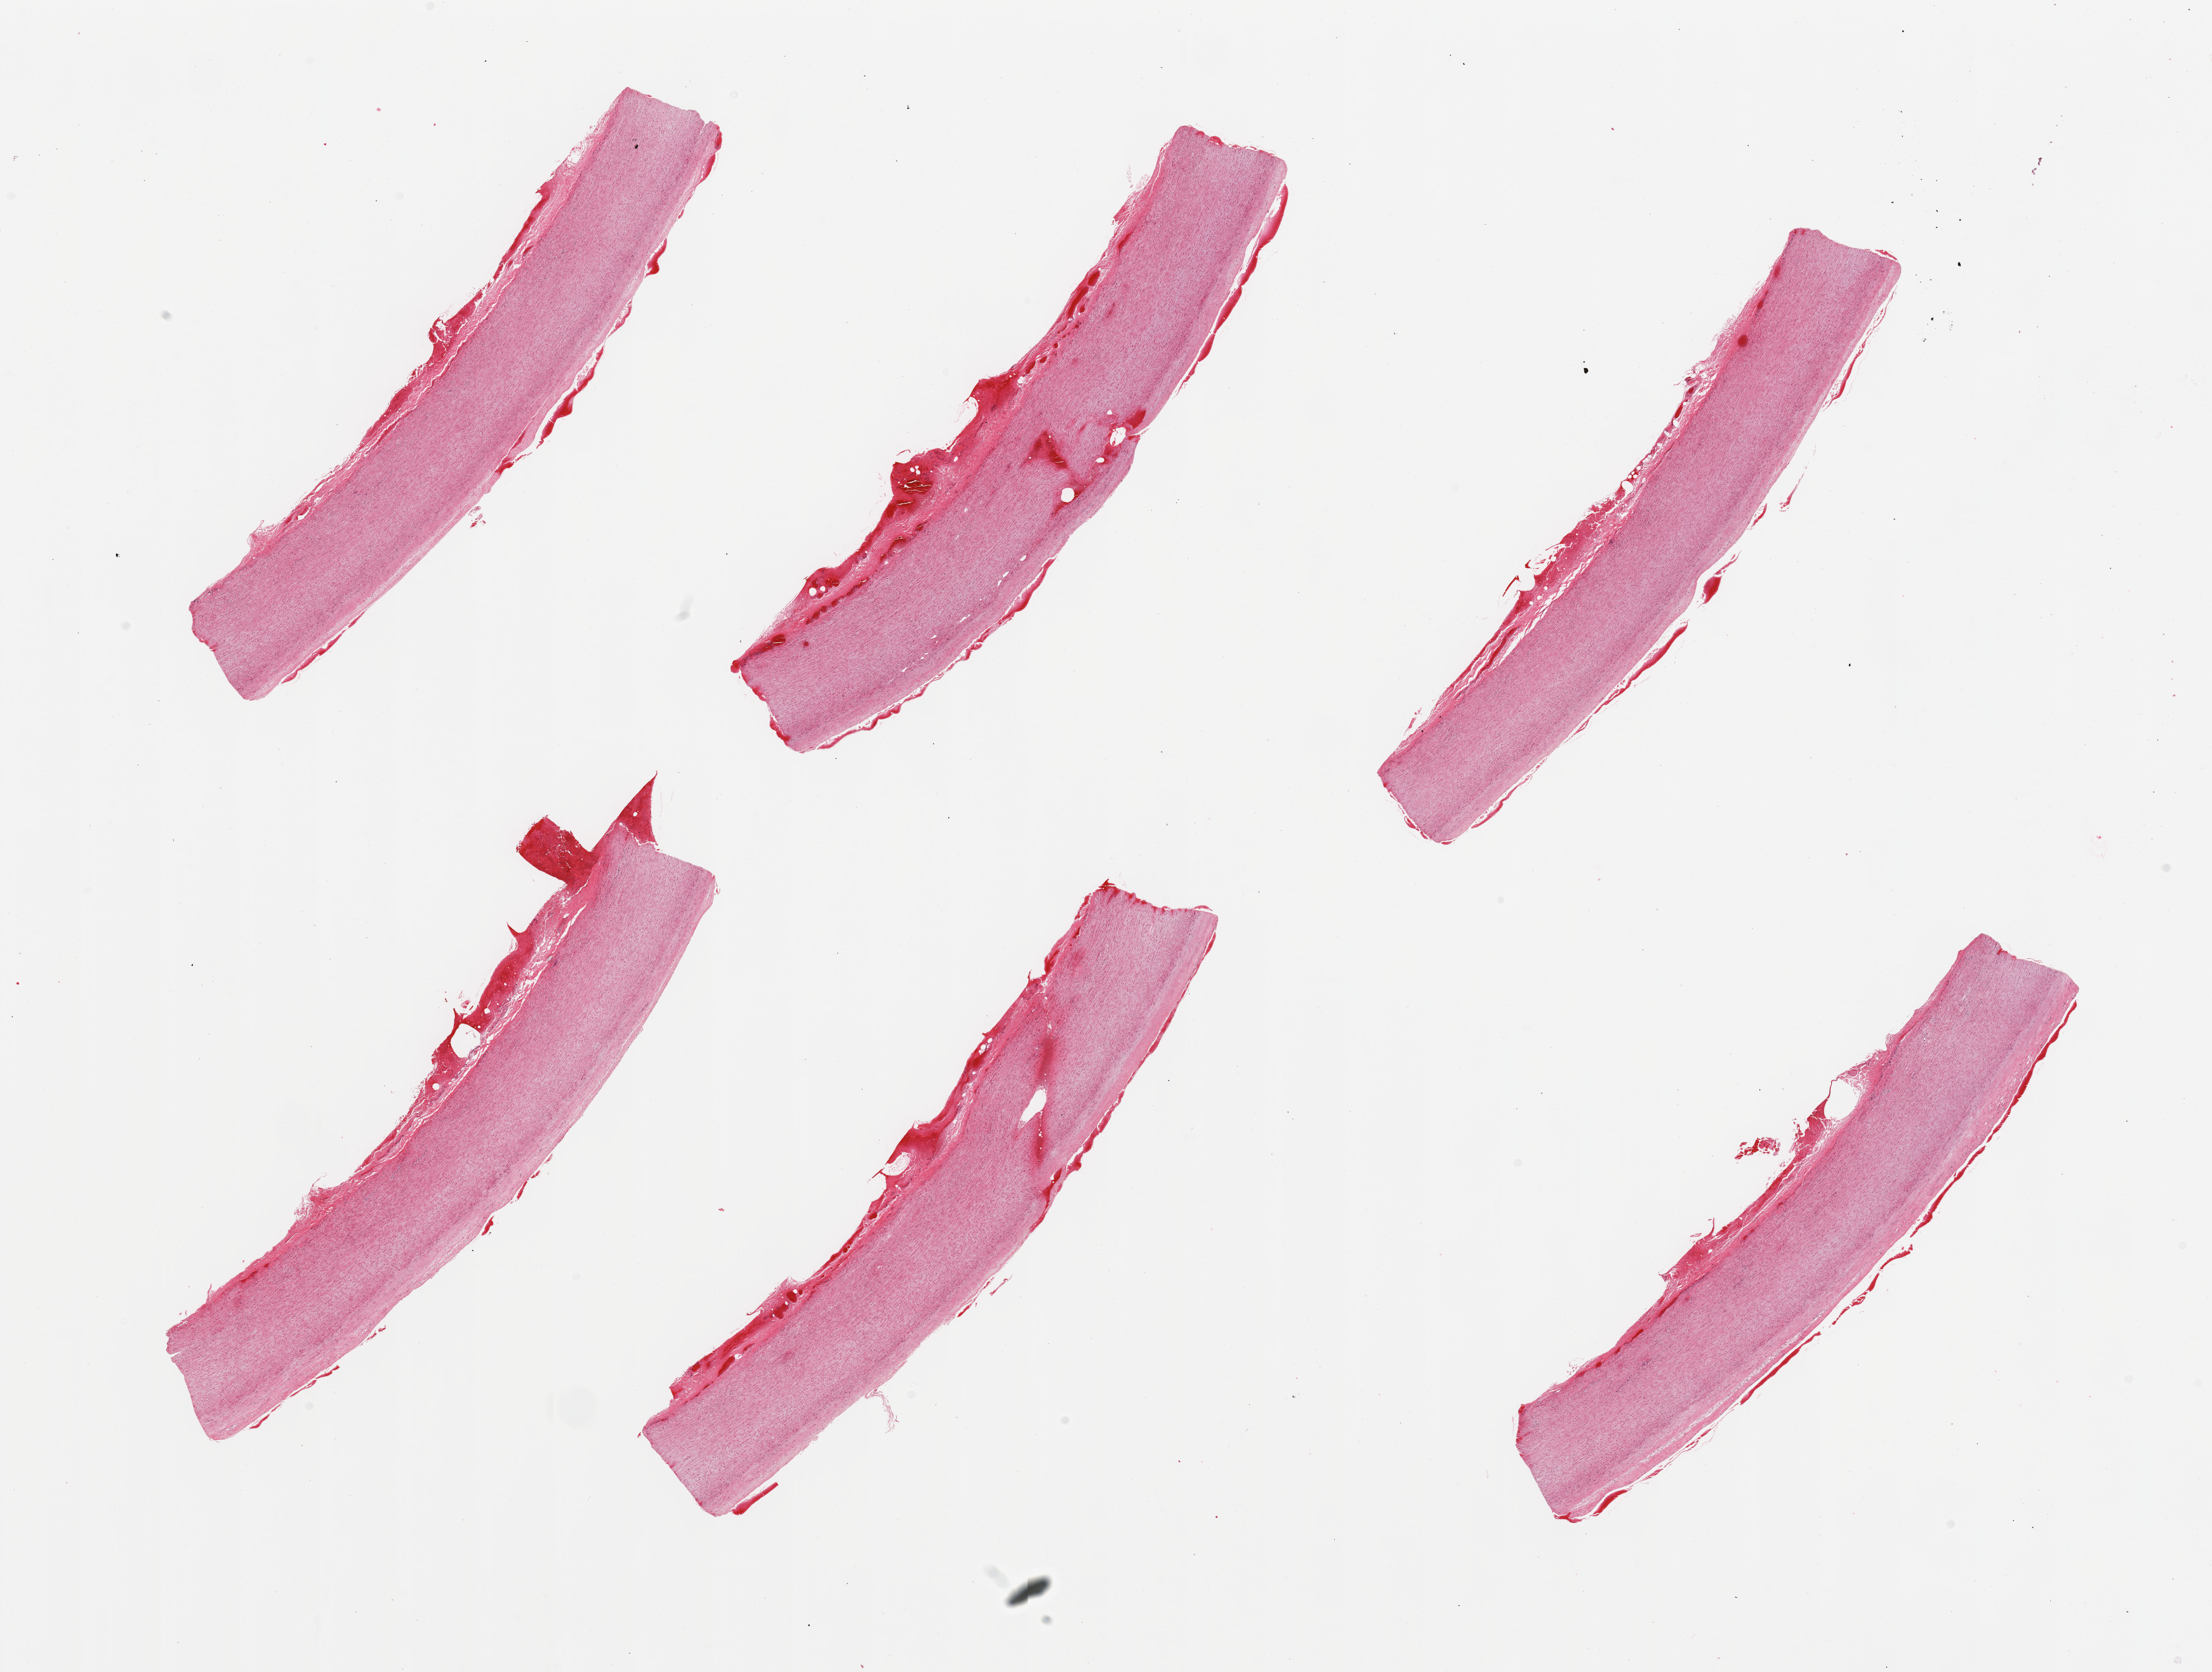
Haematoxylin and eosin whole-slide image, whole scanned area (about 27.6 x 20.8 mm, from a 20x scan) shown as a low-resolution overview, PAXgene-fixed paraffin-embedded (PFPE) section, section of aorta (target tissue), tissue donor sample. Donor: female.
Reviewer comment on this tissue sample: 6 pieces; 2 have medial hemorrhages; minimal plaque.